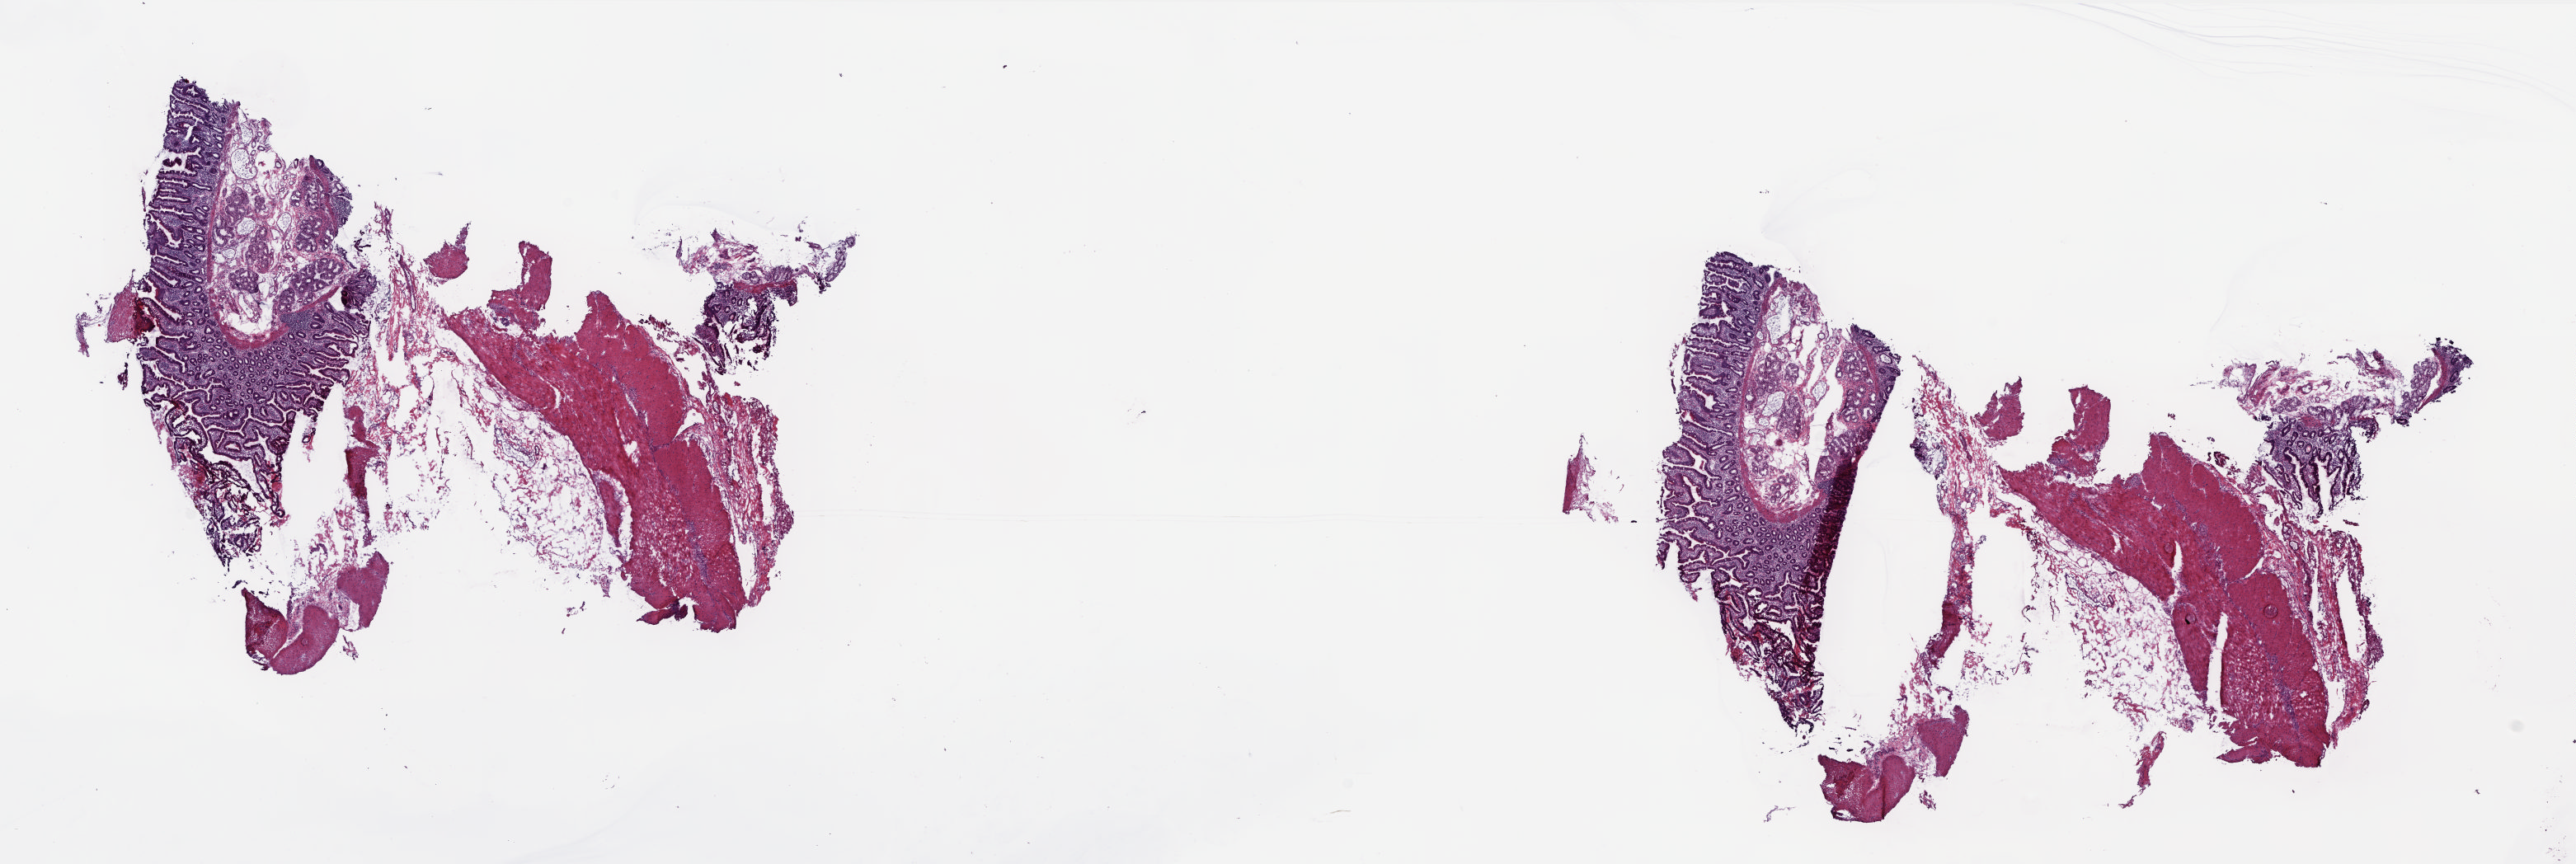
Digitized Hematoxylin and eosin (H&E) stained tissue section (whole slide) — shown as a low-resolution overview of the whole scanned area (about 25.0 x 8.4 mm); frozen section from the top of the tissue portion; sample: solid tissue normal (non-tumour tissue), pancreas. Male patient; age at initial diagnosis 66 years. Pathologist review of this section (percent, as recorded): tumour cells 0%, tumour nuclei 0%, normal cells 100%, stromal cells 0%, necrosis 0%. Inflammatory infiltration, as recorded: lymphocyte infiltration 0%, monocyte infiltration 0%, neutrophil infiltration 0%.
* this section: solid tissue normal sample (biorepository sample class)
* patient diagnosis: Infiltrating duct carcinoma, NOS (head of pancreas)